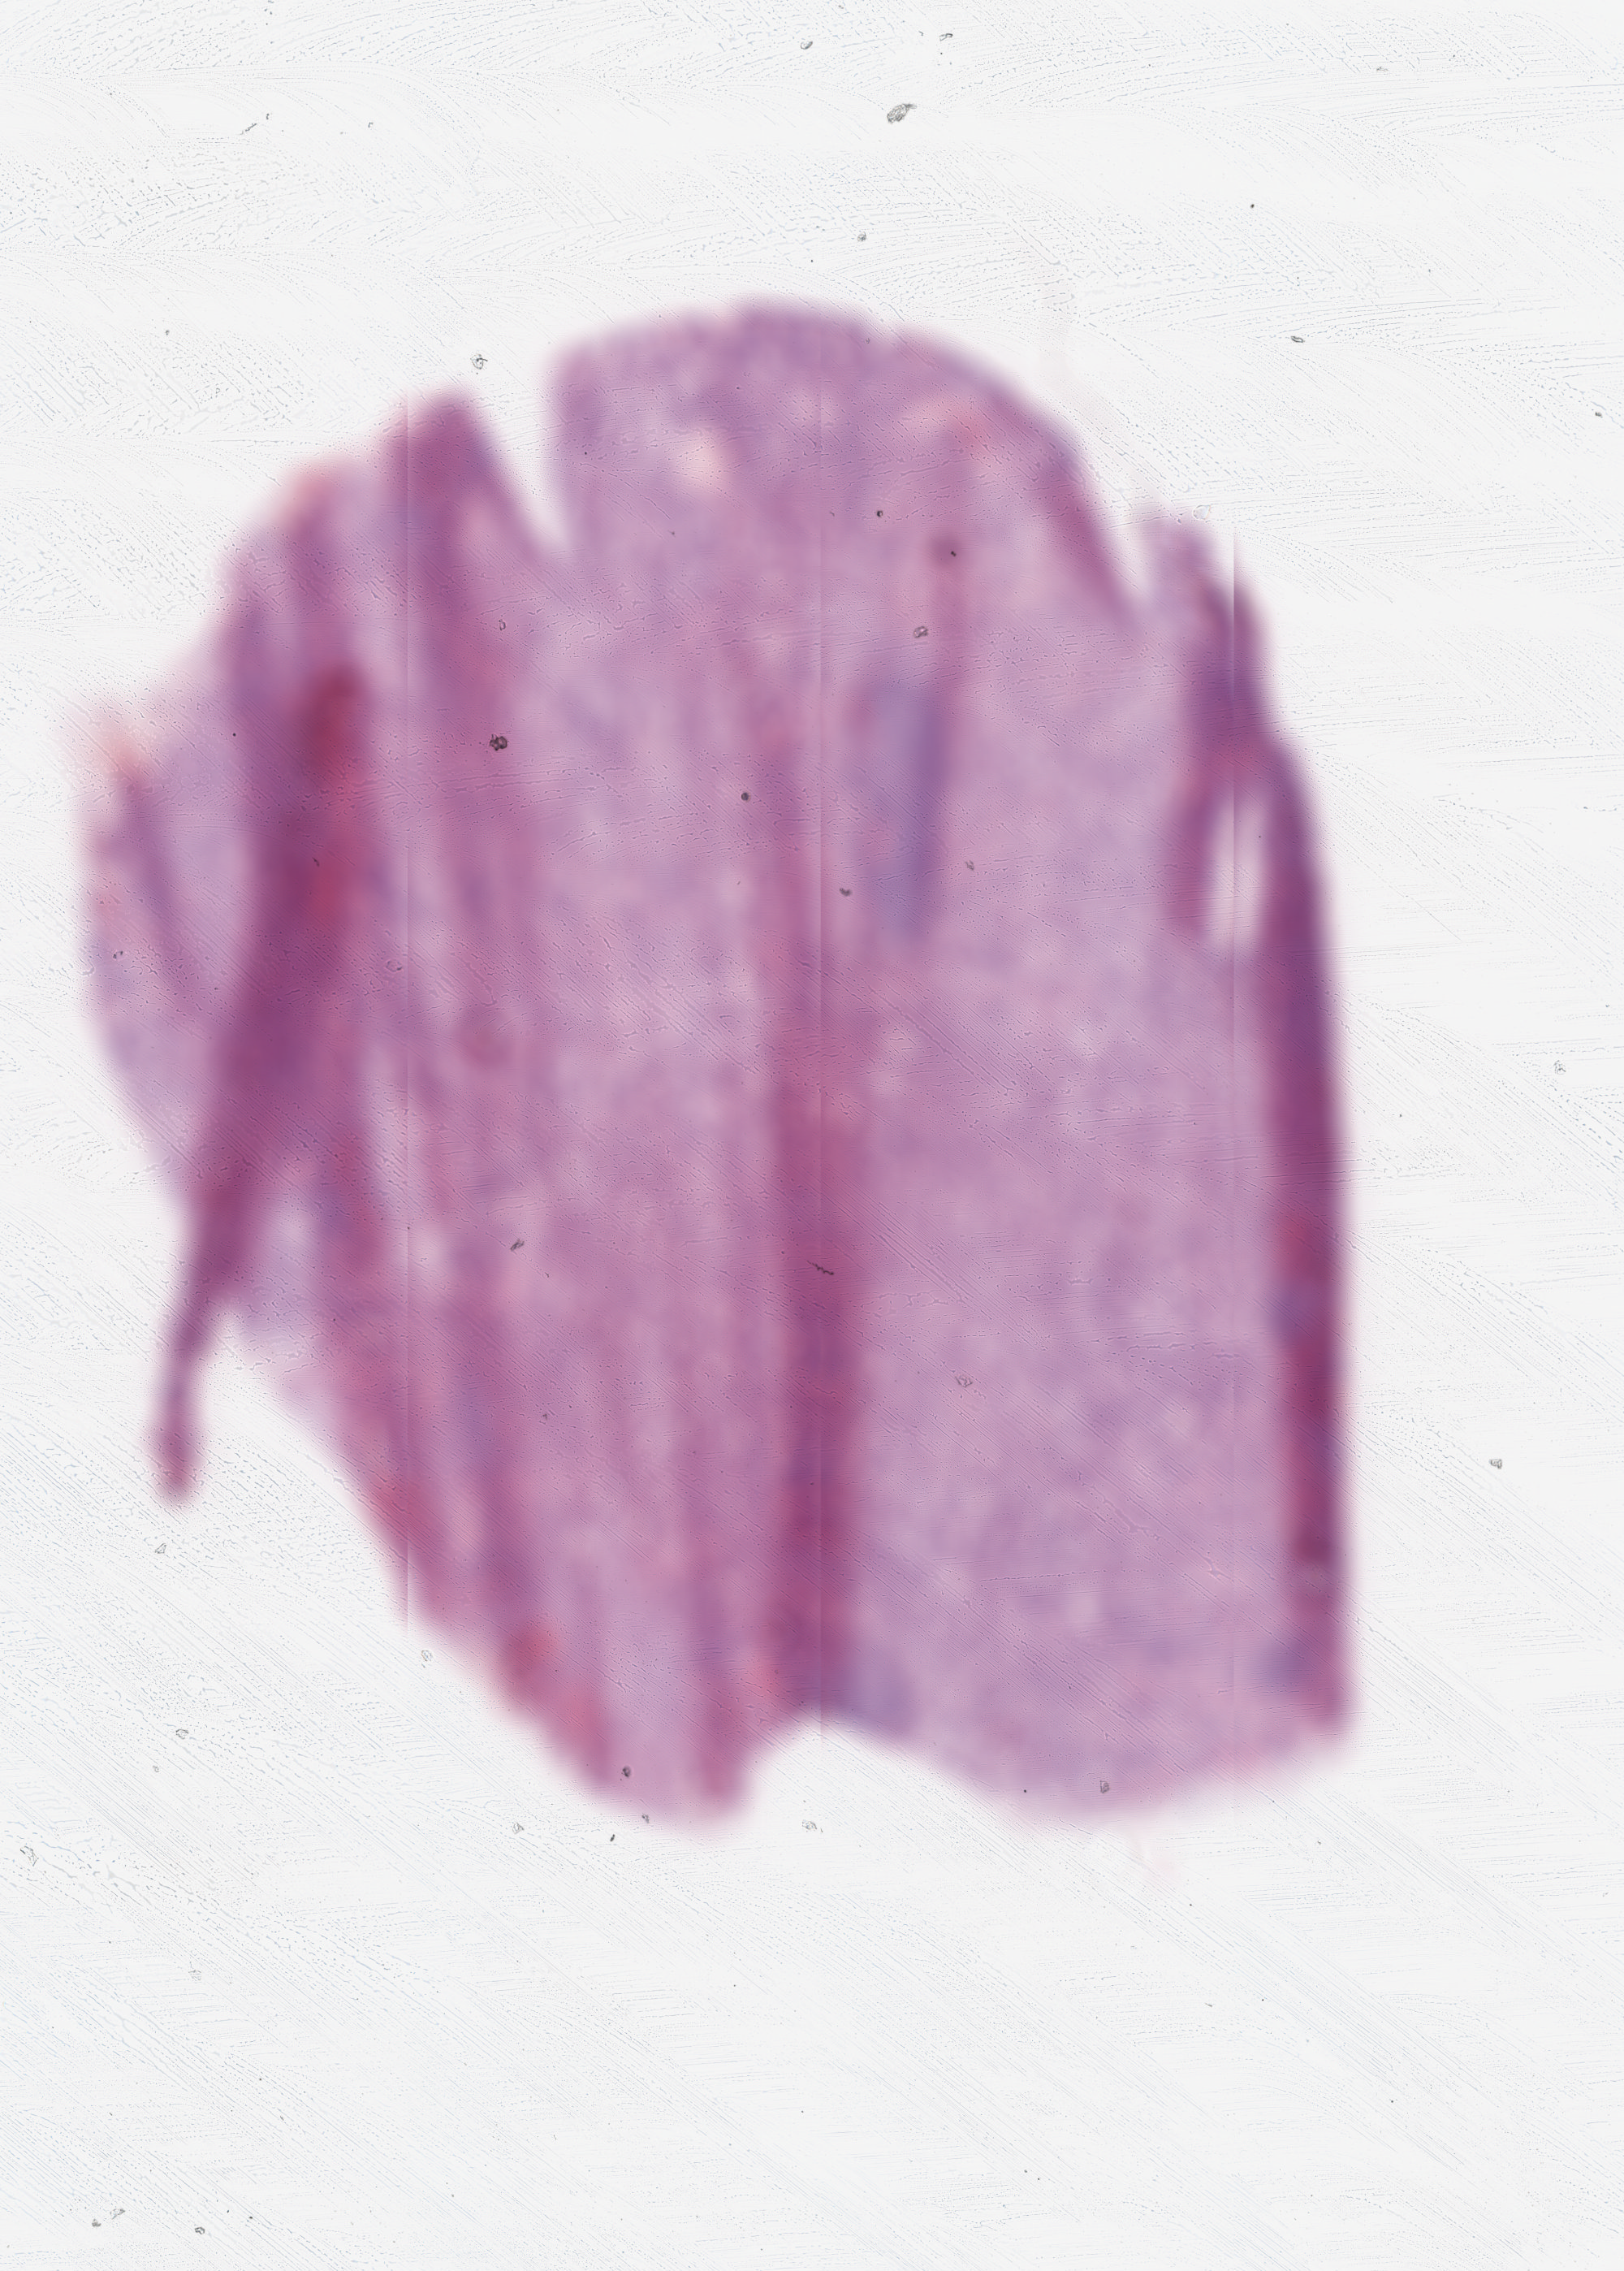
Digitized Hematoxylin and eosin (H&E) stained tissue section (whole slide), a low-resolution overview of the entire scanned area, about 4.0 x 5.6 mm (from a 20x scan); frozen section from the top of the tissue portion; sample: primary tumour, stomach. Male patient; age at initial diagnosis 80 years.
Histologic diagnosis: Tubular adenocarcinoma (body of stomach).